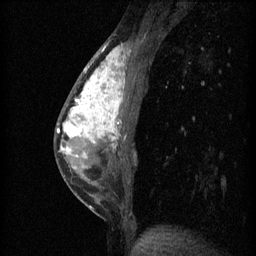
Breast MRI (dynamic contrast-enhanced), one sagittal slice. Slice 24 of 60 in the series (ordered by position). 3 images stored at this slice position (order not interpretable as contrast timing). 1.5 T. TE 4.2 ms, TR 11 ms. 256 × 256 image matrix, field of view 180 × 180 mm. Female patient, age 40 years.
Outlined on this slice (semi-automatically segmented with operator editing):
- analysis volume of interest (the breast-tissue region the enhancement analysis was run in; not a lesion): box from (x=55, y=42) to (x=143, y=203) px
- tumour enhancement mask (voxels above the 70 % enhancement threshold inside the analysis volume of interest): (x=58, y=48)–(x=130, y=159)